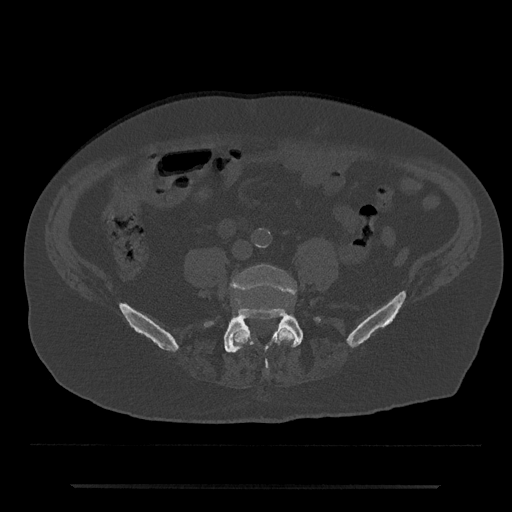
CT including the spine, one axial slice; slice 313 of 797 in the series (ordered by position); 120 kVp; bone window (W 1800 / L 400 HU); 512 × 512 image matrix, field of view 434 × 434 mm. Male patient, age 80 years. From the clinical record (not read from this slice): primary cancer: prostate; vertebrae with lytic lesions (as recorded): L1, T11.
Annotated regions visible in this slice (semi-automatically segmented with operator editing):
- L4 vertebra: bounding box <231,264,296,347> (left, top, right, bottom; pixels)
- L5 vertebra: <205,308,320,368>